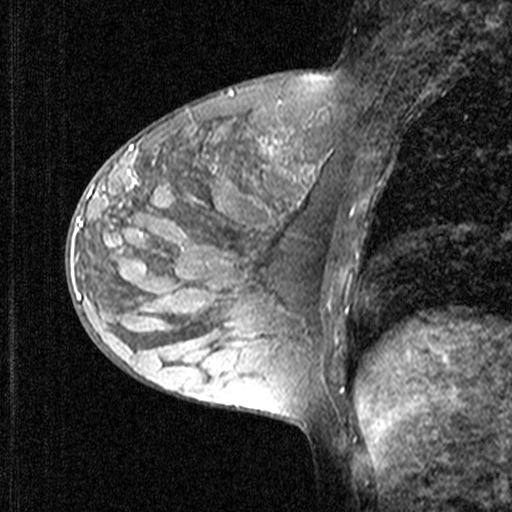
Breast MRI (dynamic contrast-enhanced), one sagittal slice; slice 18 of 44 in the series (ordered by position); dynamic contrast-enhanced study with each time point stored as its own series, time point 2 of 3 at this slice position (early post-contrast, ordered by acquisition time); 1.5 T; TE 4.5 ms, TR 11 ms; 512 × 512 image matrix. Patient: female, 27 years. Case-level facts recorded for this patient, not image findings: setting: breast cancer imaged before/during neoadjuvant chemotherapy; receptor status: HR-positive, HER2-negative.
Structures marked on this image (semi-automatically segmented with operator editing):
- analysis volume of interest (the breast-tissue region the enhancement analysis was run in; not a lesion): bounding box [x1, y1, x2, y2] px = [68, 146, 165, 239]
- tumour enhancement mask (voxels above the 90 % enhancement threshold inside the analysis volume of interest): [74, 146, 133, 235]